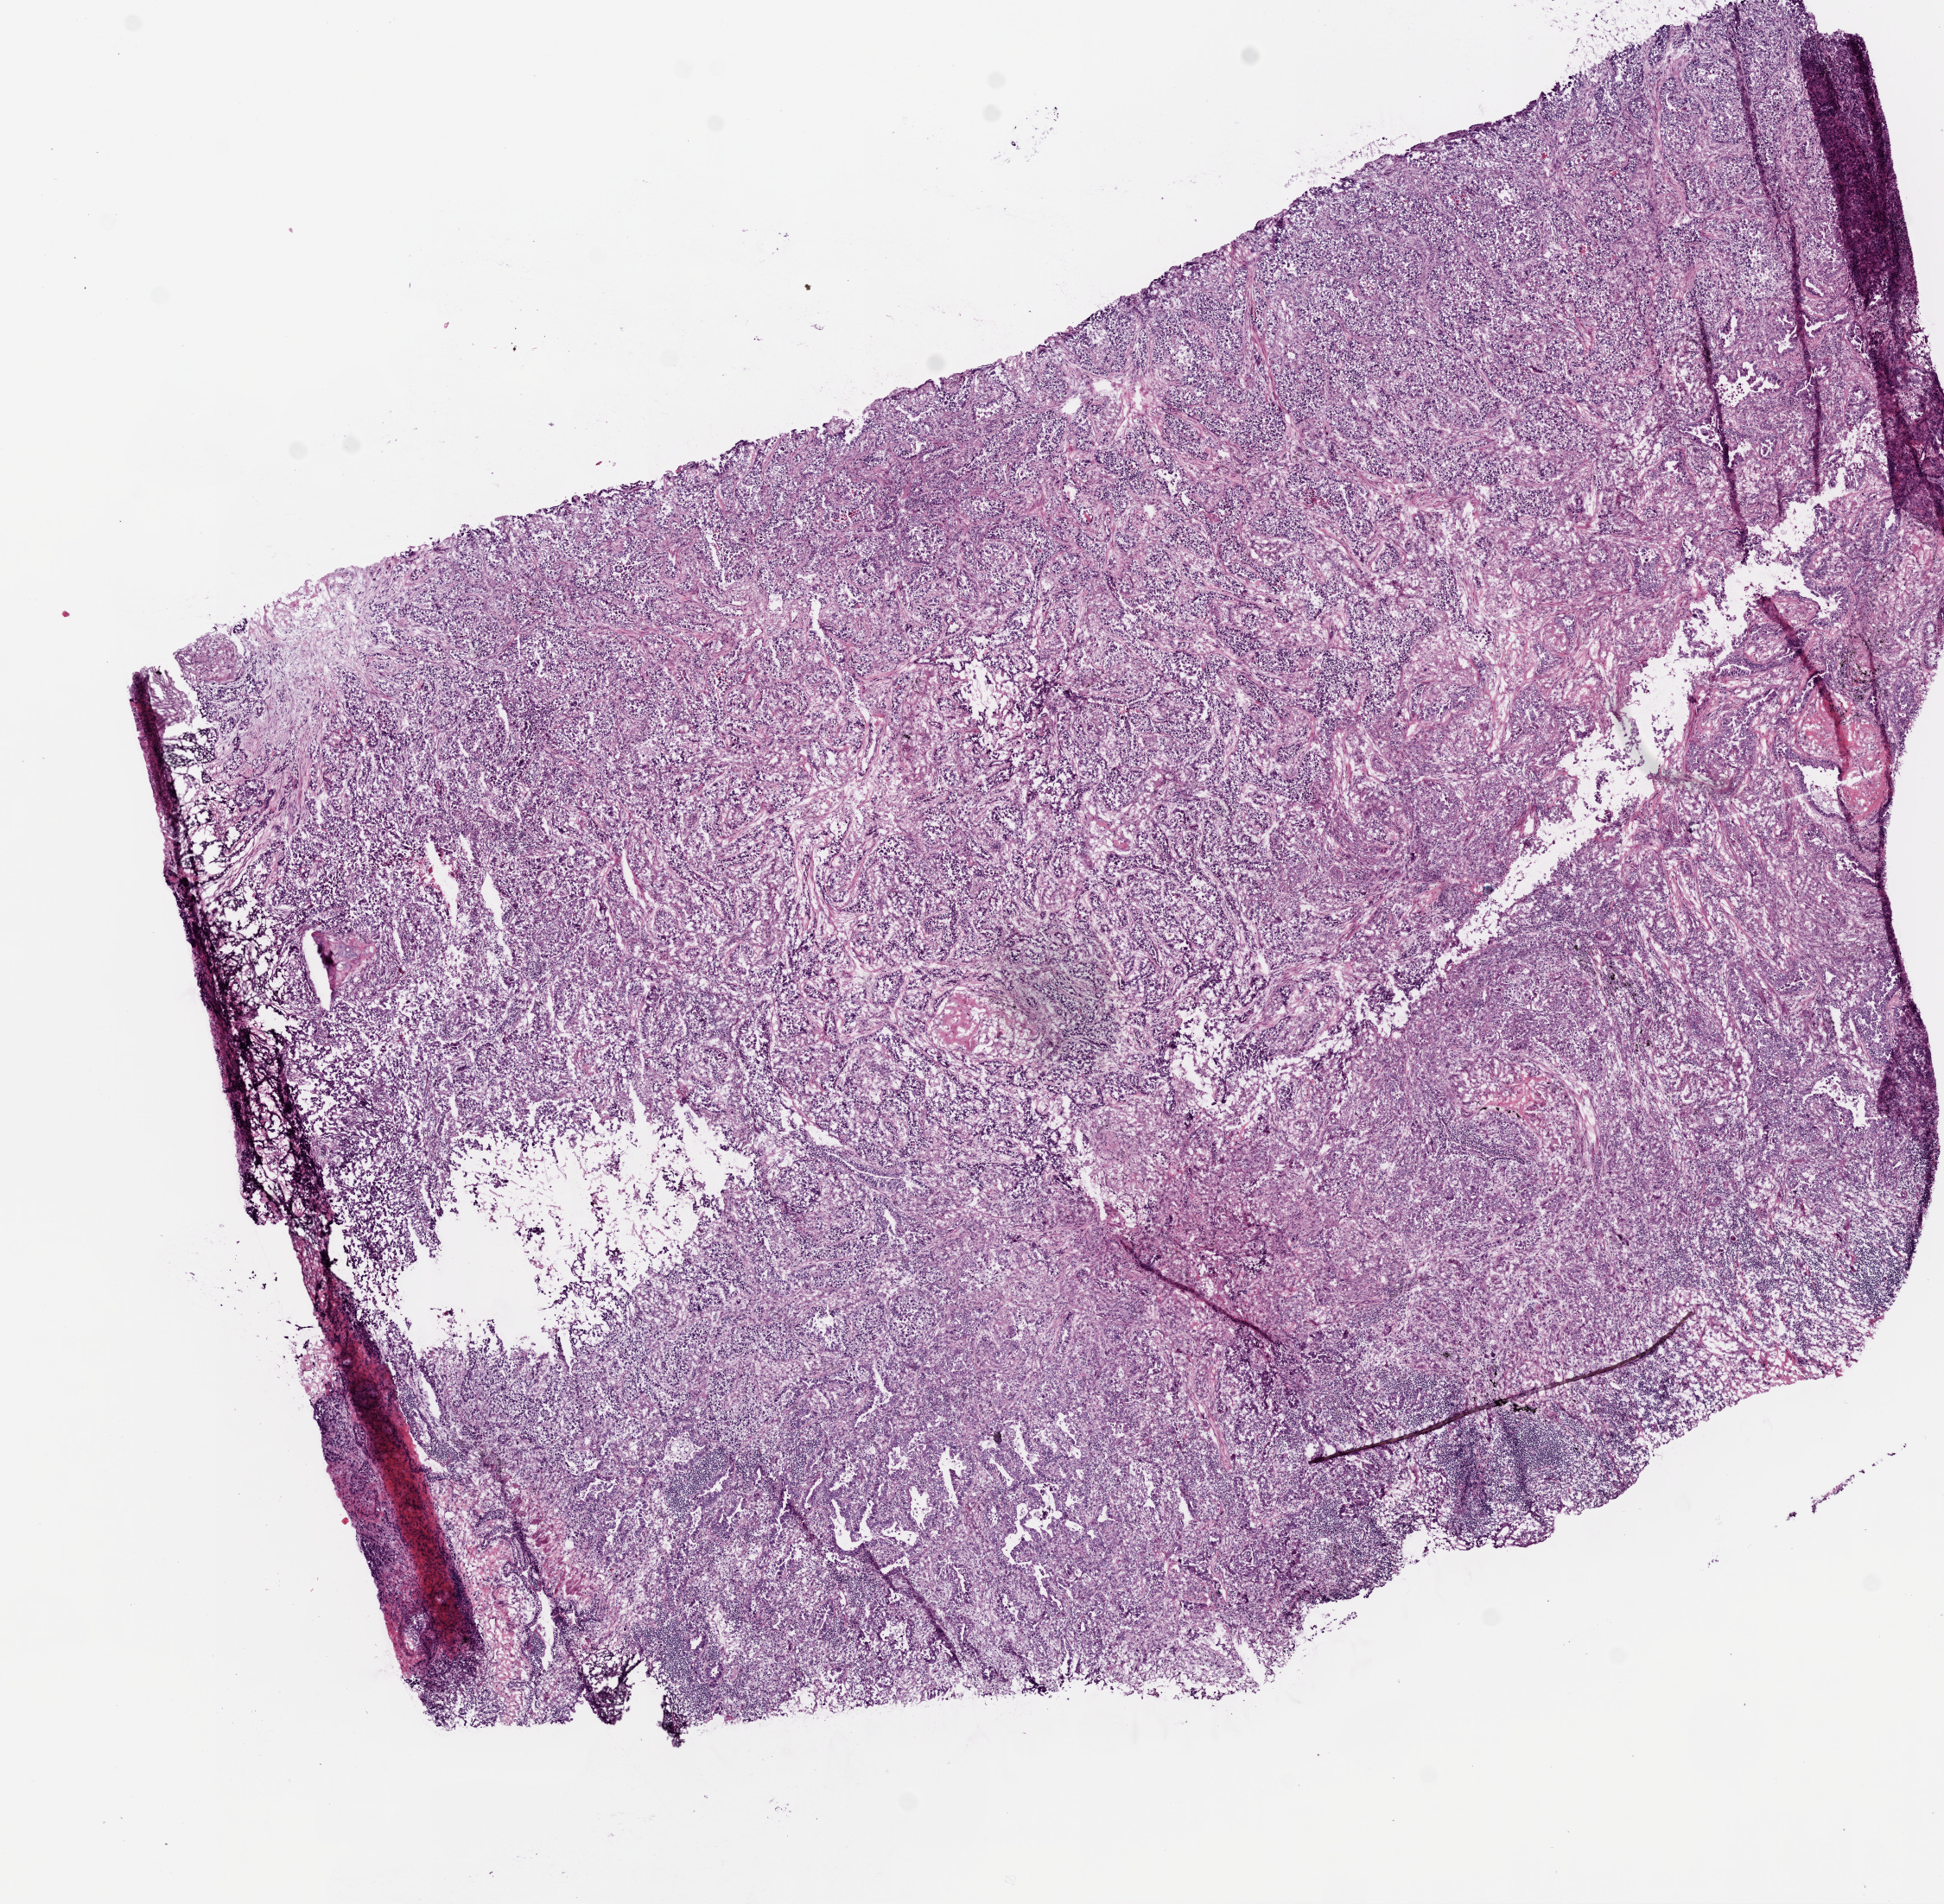
Whole-slide histology image, H&E, low-resolution overview of the scanned area, about 9.0 x 8.8 mm, frozen section from the bottom of the tissue portion, sample: primary tumour, lung. Female, age 56 years at initial diagnosis. Composition of this section per pathologist review: tumour nuclei 70%, normal cells 0%, stromal cells 15%, necrosis 5%.
AJCC pathologic stage: IV. TNM: T2 NX M1. Diagnosis: Adenocarcinoma with mixed subtypes.